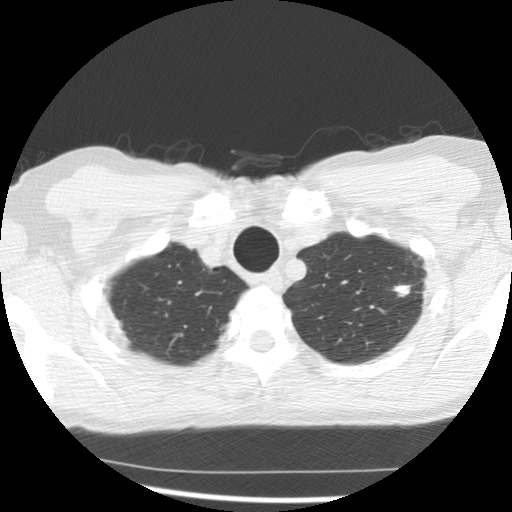
Low-dose screening chest CT, one axial slice; slice 124 of 145 in the series (ordered by position); 140 kVp; lung window (W 1500 / L -600 HU); 512 × 512 image matrix, field of view 320 × 320 mm.
Annotated regions visible in this slice (expert manual segmentation):
- lesion 2 (nodule, upper lobe of left lung): bounding box (x1, y1, x2, y2) in pixels: (392, 285, 411, 297)